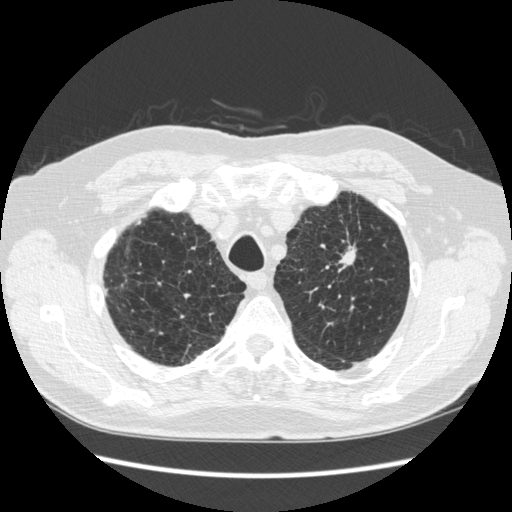
Axial slice from a low-dose chest CT screening exam. Third screening round (two years after baseline). Lung window (W 1500 / L -600 HU). 1.25 mm slice thickness. 120 kVp. Slice 46 of 267 in the series. Male, age 70 years at enrolment.
Expert reader's lesion annotation, bounding box [x1, y1, x2, y2] px = [323, 217, 374, 282]. The screening reader recorded 2 non-calcified nodules or masses ≥4 mm on this exam; which of them this box marks is not recorded. Participant outcome: lung cancer diagnosed 92 days after this screen — squamous cell carcinoma, NOS, left upper lobe, moderately differentiated (G2), stage IA (AJCC 6th edition), 18 mm at pathology.